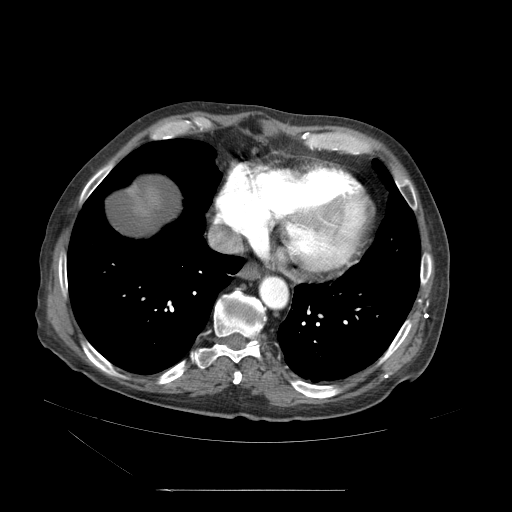
Contrast-enhanced abdominal CT (liver protocol), one axial slice. Position 60 of 71 along the scan axis. Reconstruction kernel STANDARD. 120 kVp. Soft-tissue window (W 400 / L 40 HU). 2.5 mm slice thickness. 512 × 512 image matrix. Case-level facts recorded for this patient, not image findings: diagnosis: hepatocellular carcinoma (patient treated with transarterial chemoembolisation; whether this scan precedes or follows treatment is not stated here); TNM stage (as recorded): Stage-II; Child-Pugh class: A; tumour size: 1 cm.
Structures marked on this image (semi-automatic segmentation, software-assisted and operator-edited):
- abdominal aorta: bounding box [x1, y1, x2, y2] px = [259, 273, 289, 310]
- liver parenchyma outside the tumour (the mass and vessels are separate outlines, so this box may not span the whole liver): [141, 178, 186, 231]